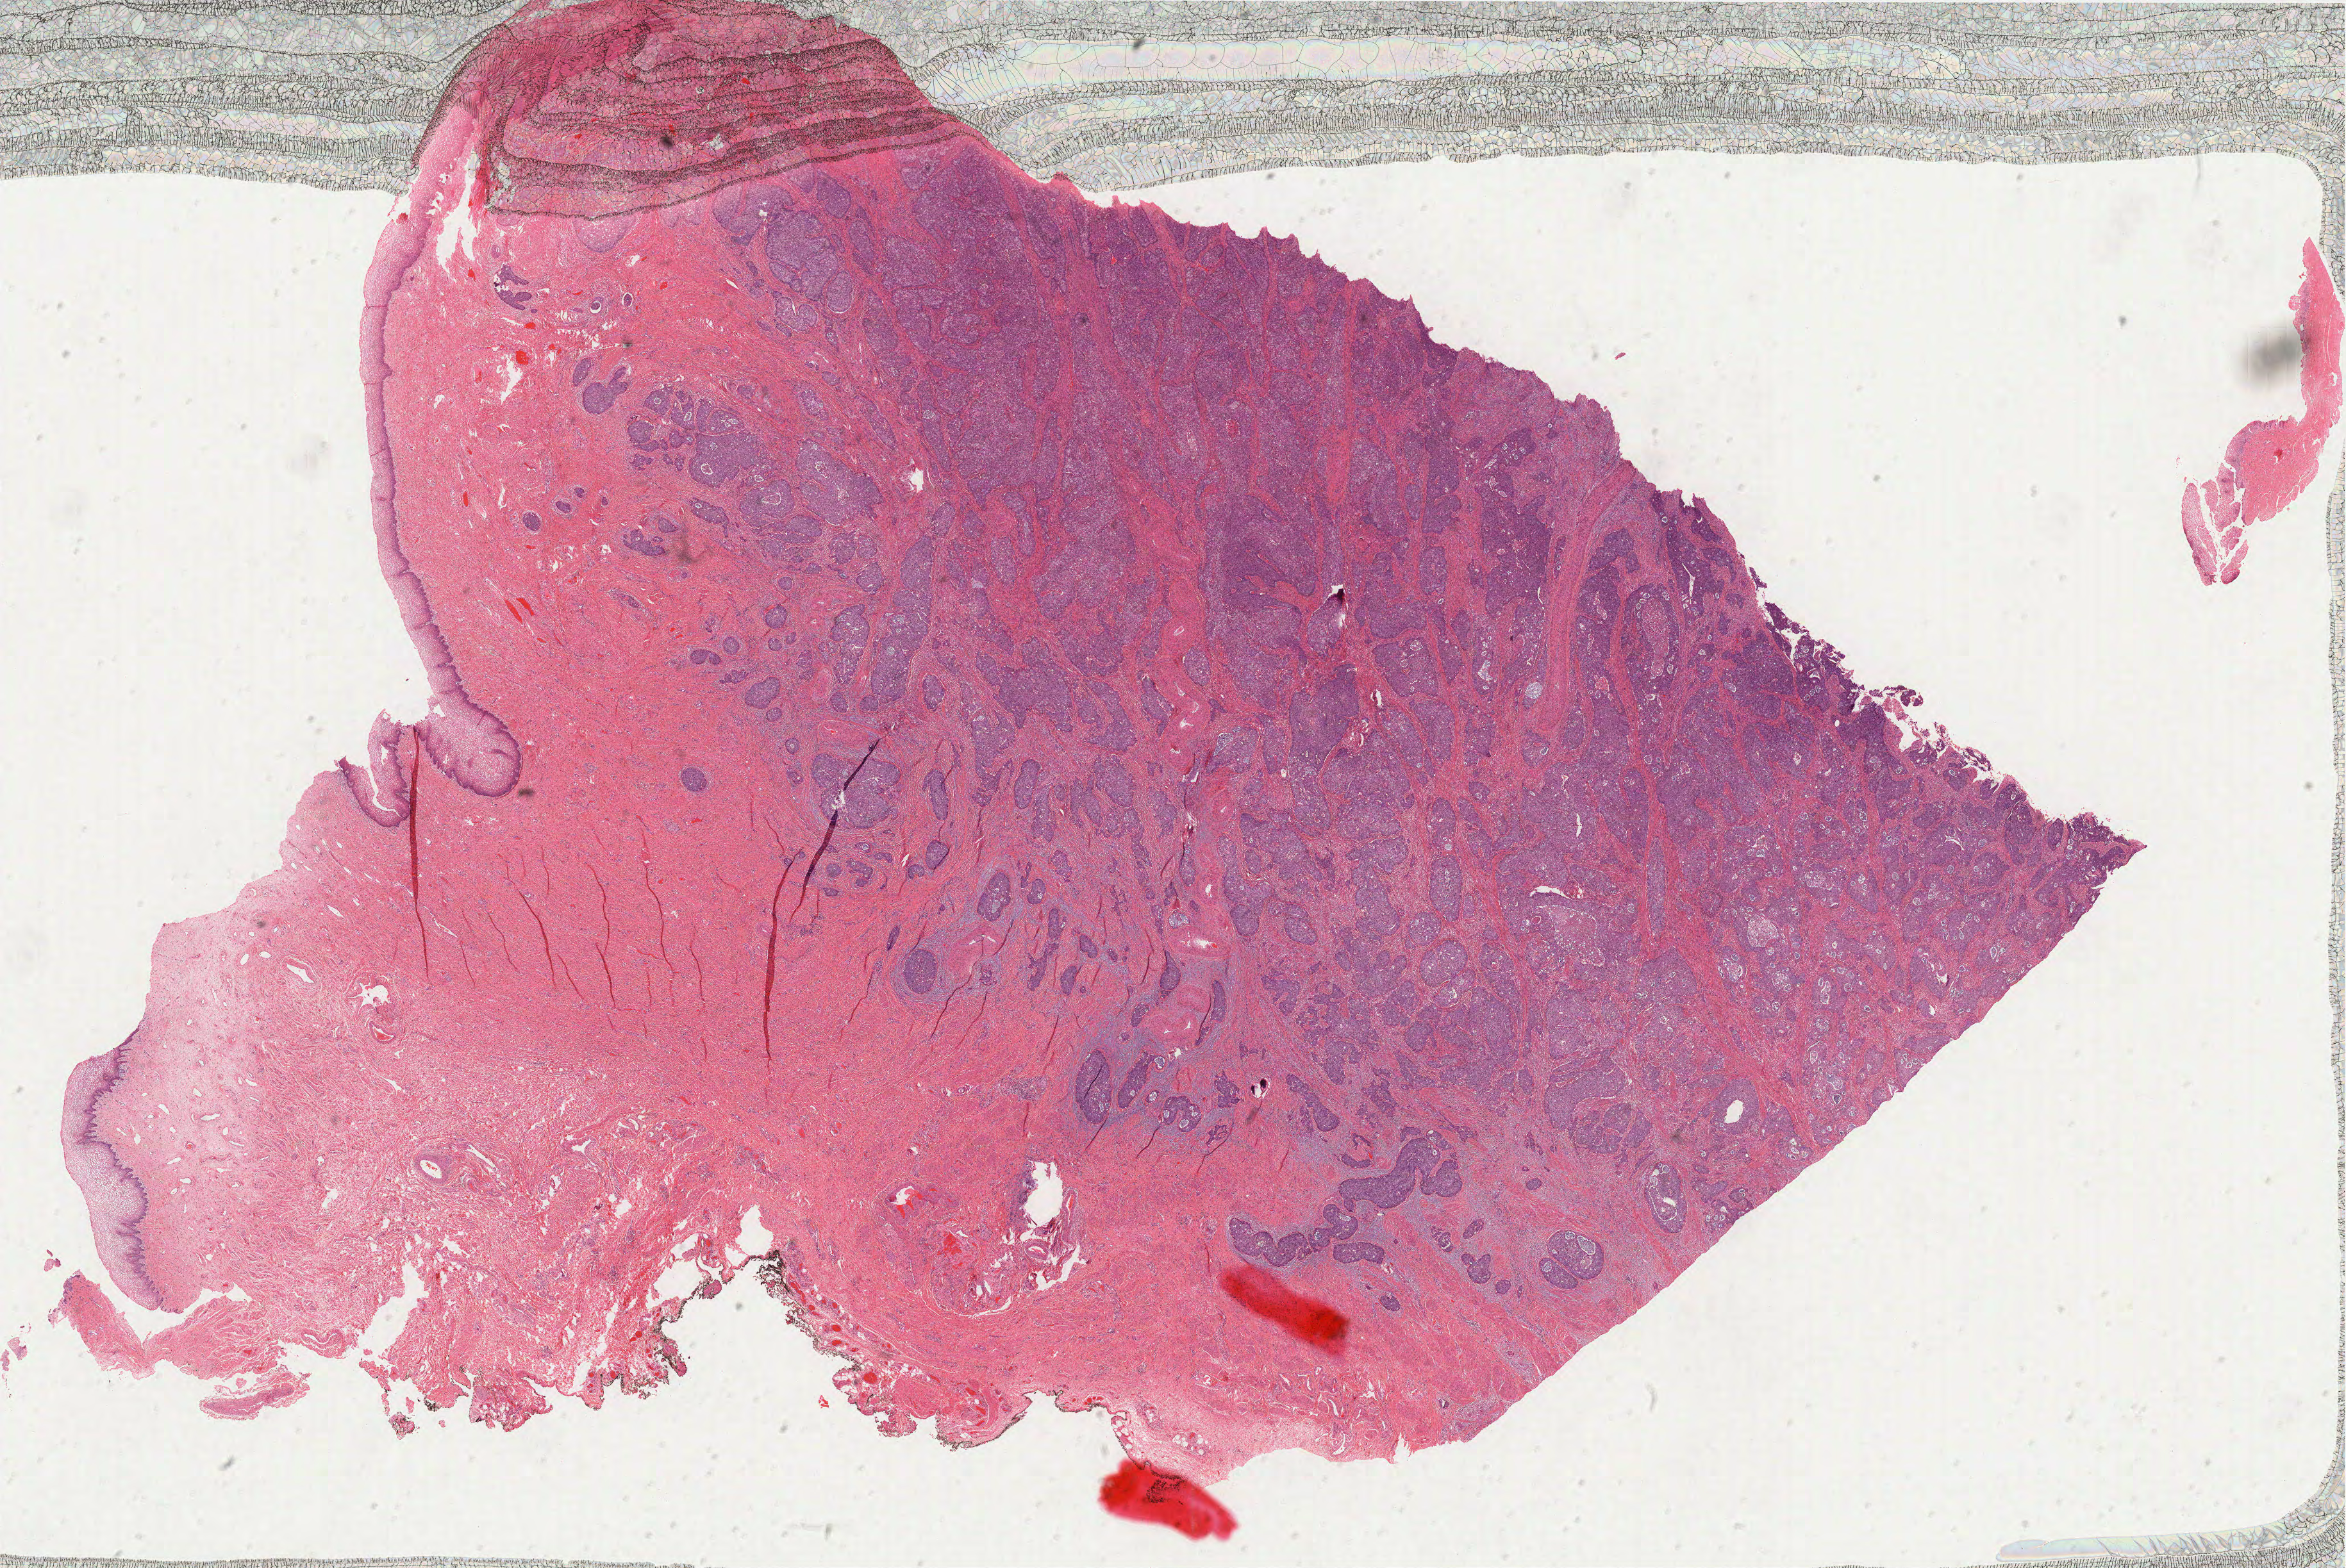
H&E-stained whole-slide image — shown as a low-resolution overview of the whole scanned area (about 29.3 x 19.6 mm, acquisition: 40x scan); formalin-fixed paraffin-embedded (FFPE) diagnostic section; primary tumour sample from the cervix. Female patient; age at initial diagnosis 35 years. Histologic grade: G2 (moderately differentiated).
FIGO stage: IB1. Diagnosis: Mucinous adenocarcinoma, endocervical type (cervix uteri). Lymph nodes positive (case pathology): 1 of 27 examined.